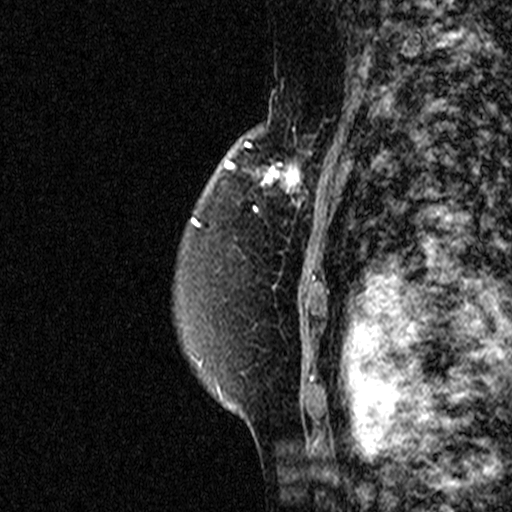
Breast MRI (dynamic contrast-enhanced), one sagittal slice. Position 32 of 44 along the scan axis. Dynamic contrast-enhanced study with each time point stored as its own series, time point 2 of 3 at this slice position (early post-contrast, ordered by acquisition time). 1.5 T. TE 4.5 ms, TR 11 ms. 512 × 512 image matrix. Female patient, age 49 years. Case-level facts recorded for this patient, not image findings: setting: breast cancer imaged before/during neoadjuvant chemotherapy; receptor status: triple-negative.
Annotated regions visible in this slice (semi-automatic segmentation, software-assisted and operator-edited):
- analysis volume of interest (the breast-tissue region the enhancement analysis was run in; not a lesion): bounding box <257,122,331,227> (left, top, right, bottom; pixels)
- tumour enhancement mask (voxels above the 90 % enhancement threshold inside the analysis volume of interest): <262,158,307,197>